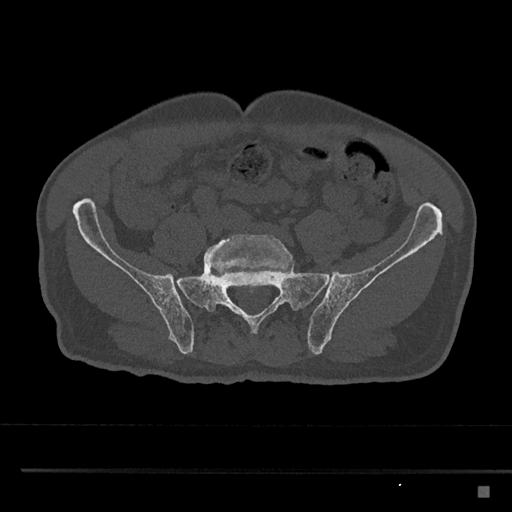
CT including the spine, one axial slice. Position 550 of 797 along the scan axis. Reconstruction kernel Br40s/3. Bone window (W 1800 / L 400 HU). 0.5 mm slice thickness. 512 × 512 image matrix, field of view 391 × 391 mm. Male patient, age 59 years. Case-level facts recorded for this patient, not image findings: primary cancer: prostate.
Structures marked on this image (semi-automatic segmentation, software-assisted and operator-edited):
- L5 vertebra: box from (x=203, y=234) to (x=292, y=276) px